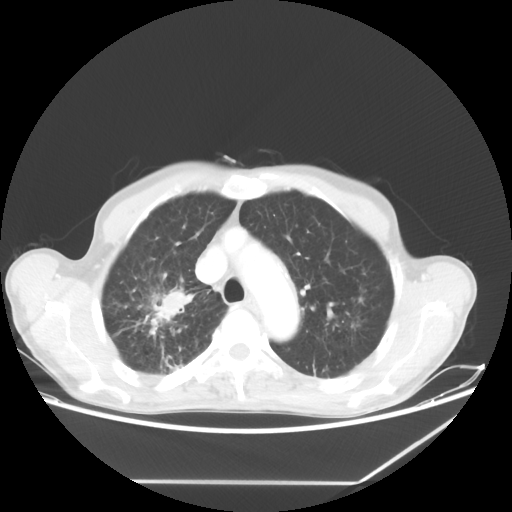
Chest CT, one axial slice. Slice 48 of 65 in the series (ordered by position). Reconstruction kernel STANDARD. 80 kVp. Lung window (W 1500 / L -600 HU). 5 mm slice thickness. 512 × 512 image matrix, field of view 397 × 397 mm. Patient: male, 68 years. From the clinical record (not read from this slice): clinical TNM (as recorded): T3 N3 M0.
Outlined on this slice (bounding box drawn by a radiologist):
- lung tumour (recorded histology: adenocarcinoma): box from (x=144, y=273) to (x=192, y=342) px